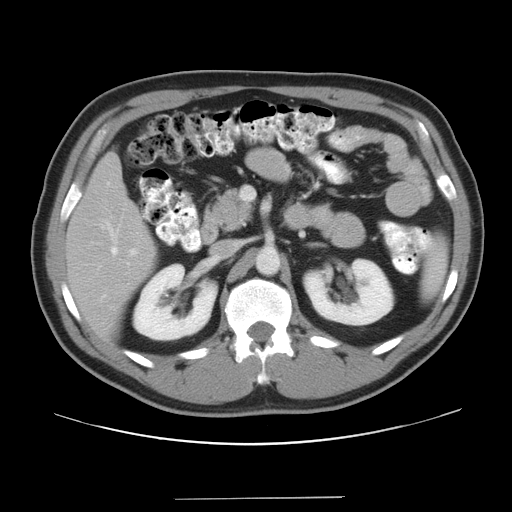
Contrast-enhanced abdominal CT, one axial slice. Position 19 of 37 along the scan axis. Intravenous contrast given. Soft-tissue window (W 400 / L 40 HU). 7.5 mm slice thickness. 512 × 512 image matrix. Male patient, age 46 years. Case-level facts recorded for this patient, not image findings: diagnosis: colorectal cancer liver metastases, imaged before liver resection; multiple liver metastases: yes; largest metastasis: 1 cm.
Structures marked on this image (manually delineated by an expert):
- hepatic veins: bounding box <111,247,129,265> (left, top, right, bottom; pixels)
- liver: <67,156,155,335>
- planned liver remnant (the part of the liver to remain after resection): <67,156,155,336>
- portal vein (with intrahepatic branches): <131,249,136,255>